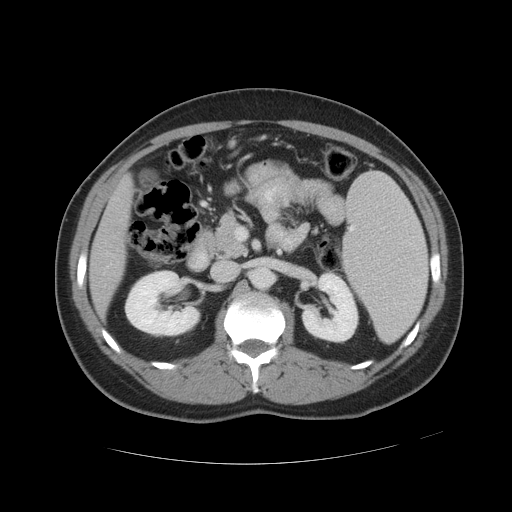
Contrast-enhanced abdominal CT, one axial slice. Position 23 of 49 along the scan axis. 120 kVp. Intravenous contrast given. Soft-tissue window (W 400 / L 40 HU). 512 × 512 image matrix. Male patient, age 42 years. From the clinical record (not read from this slice): diagnosis: colorectal cancer liver metastases, imaged before liver resection; multiple liver metastases: yes; largest metastasis: 2.8 cm; disease in both lobes: yes.
Outlined on this slice (outlined manually by an expert reader):
- liver: box from (x=91, y=182) to (x=131, y=314) px
- planned liver remnant (the part of the liver to remain after resection): (x=91, y=235)–(x=124, y=314)